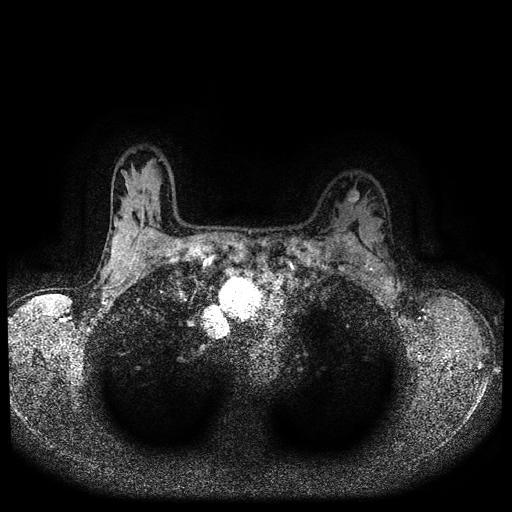
Breast MRI (dynamic contrast-enhanced, multi-phase), one axial slice. Position 77 of 116 along the scan axis. Dynamic contrast-enhanced series, time point 2 of 5 at this slice position (early post-contrast). 1.5 T. TE 2.7 ms, TR 5.4 ms. 2 mm slice thickness. 512 × 512 image matrix. Female patient, age 32 years.
Annotated regions visible in this slice (semi-automatic segmentation, software-assisted and operator-edited):
- breast lesion (labelled benign in the annotation): box from (x=345, y=187) to (x=360, y=207) px